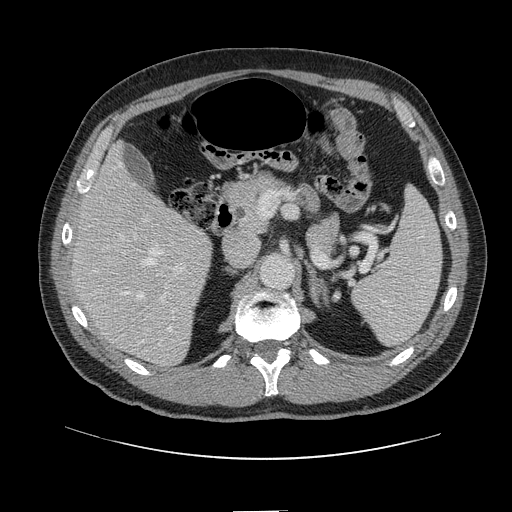
Contrast-enhanced abdominal CT, one axial slice. Slice 72 of 161 in the series (ordered by position). Soft-tissue window (W 400 / L 40 HU). 2.5 mm slice thickness. 512 × 512 image matrix, field of view 412 × 412 mm. Male patient, age 66 years. From the clinical record (not read from this slice): diagnosis: colorectal cancer liver metastases, imaged before liver resection; multiple liver metastases: no; largest metastasis: 3.5 cm; disease in both lobes: no.
Annotated regions visible in this slice (manually delineated by an expert):
- hepatic veins: bounding box <119,162,172,330> (left, top, right, bottom; pixels)
- liver: <73,149,212,365>
- planned liver remnant (the part of the liver to remain after resection): <72,148,190,292>
- portal vein (with intrahepatic branches): <122,217,186,304>